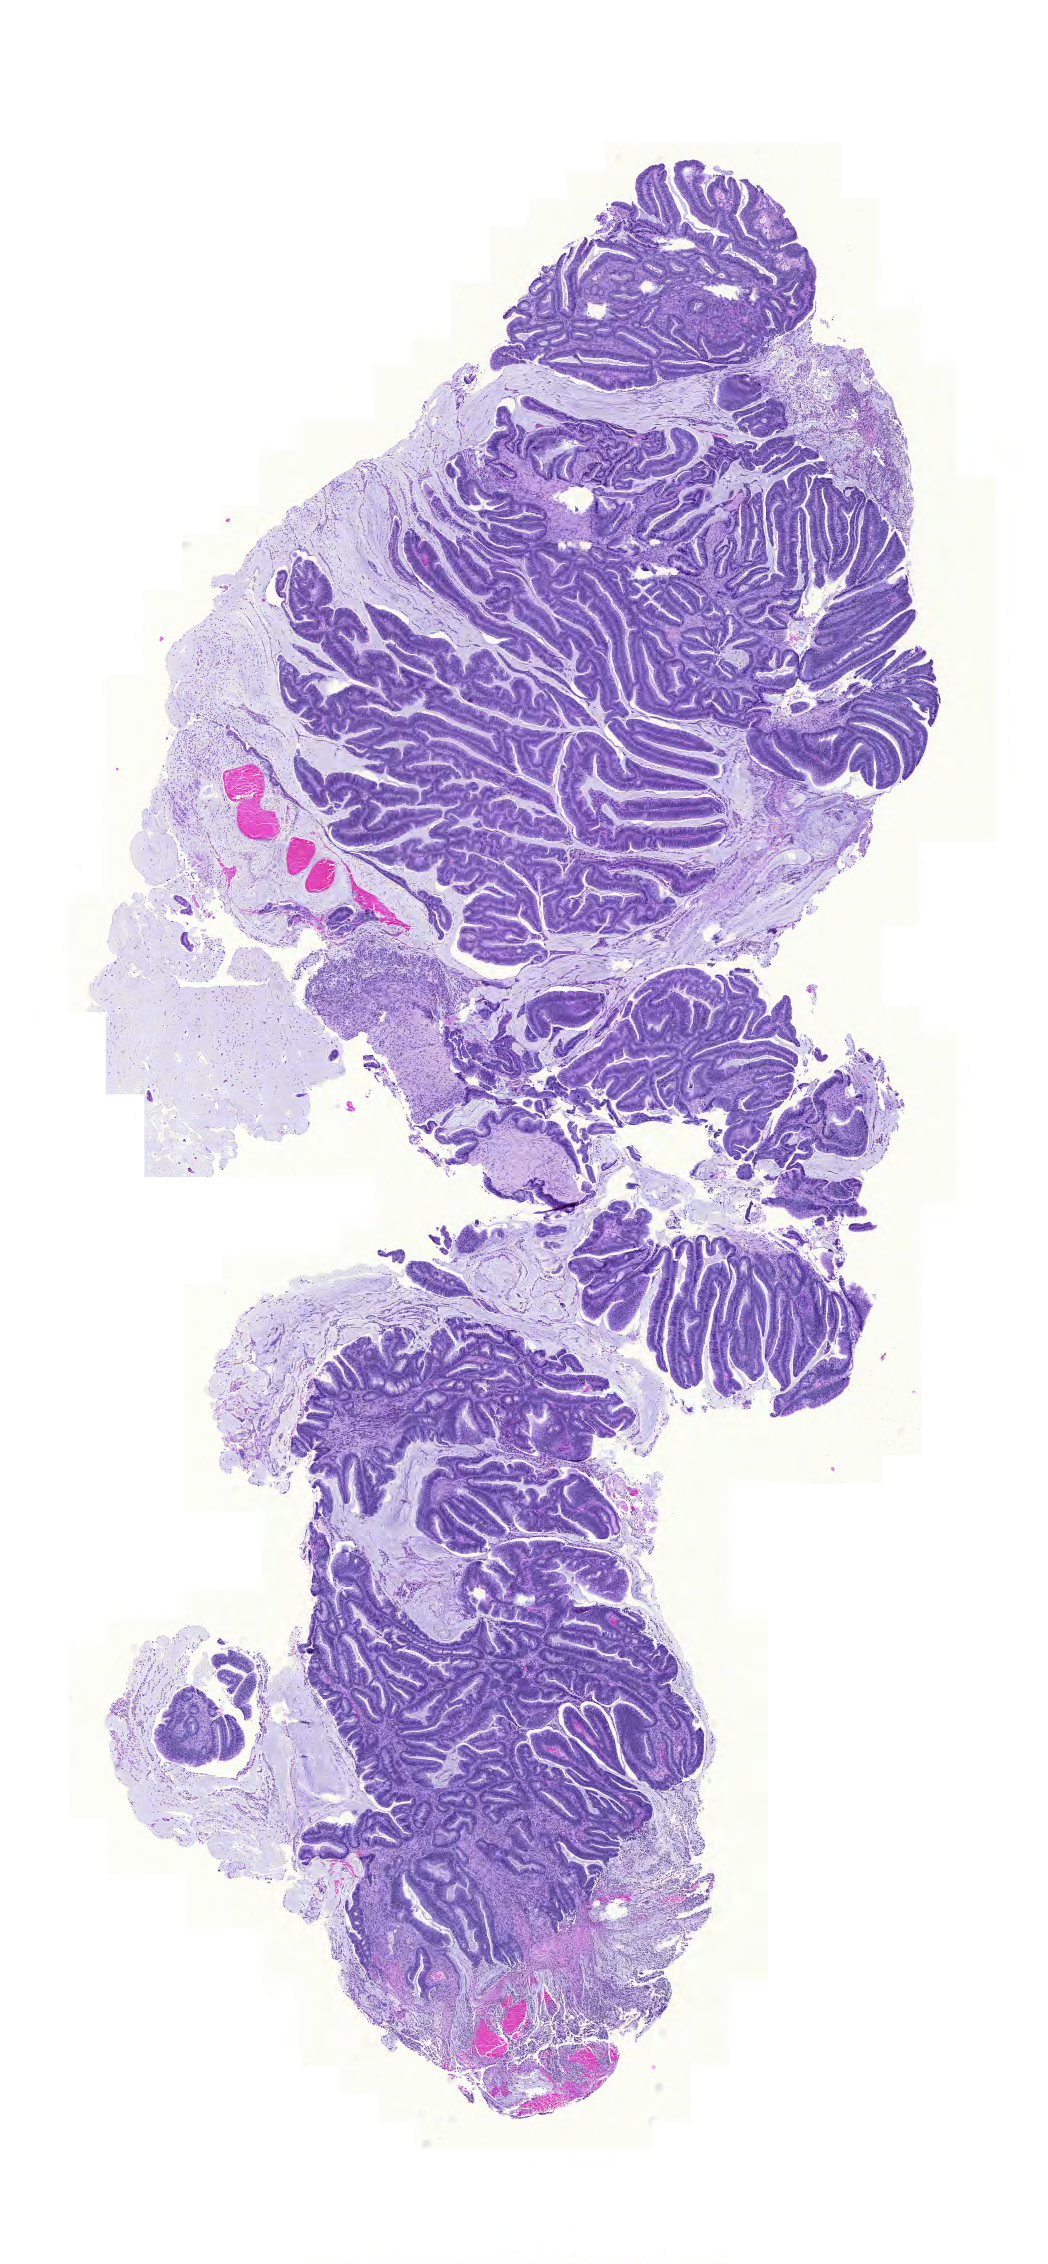
H&E-stained whole-slide image — low-resolution overview of the scanned area, about 7.8 x 16.8 mm; formalin-fixed paraffin-embedded (FFPE) diagnostic section; sample: primary tumour, colon. Patient: female, age at initial diagnosis 81 years.
Diagnosis: Adenocarcinoma, NOS.